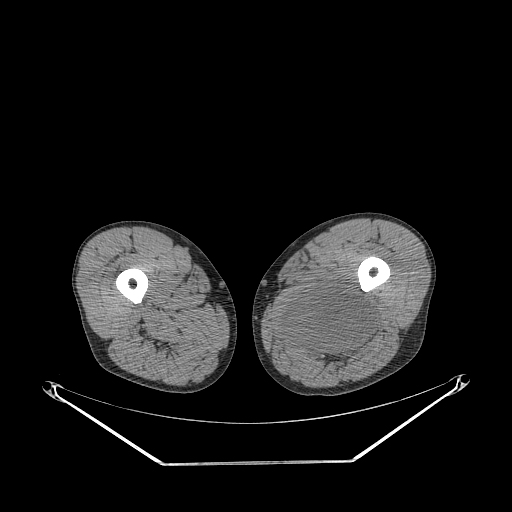
CT of an extremity soft-tissue mass (from a PET/CT study), one axial slice; position 246 of 267 along the scan axis; soft-tissue window (W 400 / L 40 HU); 3.75 mm slice thickness; 512 × 512 image matrix, field of view 500 × 500 mm. Male patient. From the clinical record (not read from this slice): histological type: undifferentiated pleomorphic liposarcoma; grade: high; site of the primary tumour: left thigh.
Outlined on this slice (expert contour drawn on MRI and transferred to this co-registered scan by the dataset authors):
- gross tumour volume including surrounding oedema: bounding box (x1, y1, x2, y2) in pixels: (278, 286, 375, 362)
- gross tumour volume (mass): (286, 286, 375, 352)